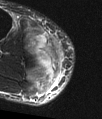
MRI of an extremity soft-tissue mass, one axial slice; position 35 of 48 along the scan axis; T2-weighted fat-saturated; MR volume resampled by the dataset authors to the PET/CT grid (not the native acquisition matrix); 3.27 mm slice thickness; 102 × 119 image matrix, field of view 100 × 116 mm. Male patient. Case-level facts recorded for this patient, not image findings: histological type: pleiomorphic liposarcoma; grade: high; site of the primary tumour: right calf.
Outlined on this slice (expert contour drawn on MRI and transferred to this co-registered scan by the dataset authors):
- gross tumour volume including surrounding oedema: bounding box (x1, y1, x2, y2) in pixels: (28, 33, 63, 77)
- gross tumour volume (mass): (39, 46, 56, 61)